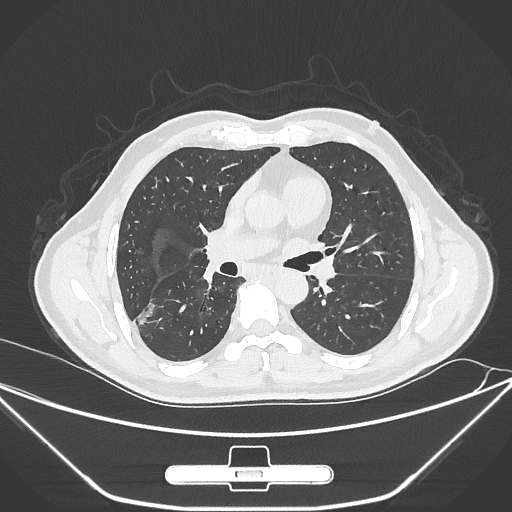
Chest CT, one axial slice. Position 158 of 310 along the scan axis. 120 kVp. Lung window (W 1500 / L -600 HU). 1 mm slice thickness. 512 × 512 image matrix, field of view 398 × 398 mm. Male patient, age 71 years. Case-level facts recorded for this patient, not image findings: clinical TNM (as recorded): T1c N0 M0.
Outlined on this slice (bounding box drawn by a radiologist):
- lung tumour (recorded histology: adenocarcinoma): bounding box (x1, y1, x2, y2) in pixels: (136, 294, 163, 336)